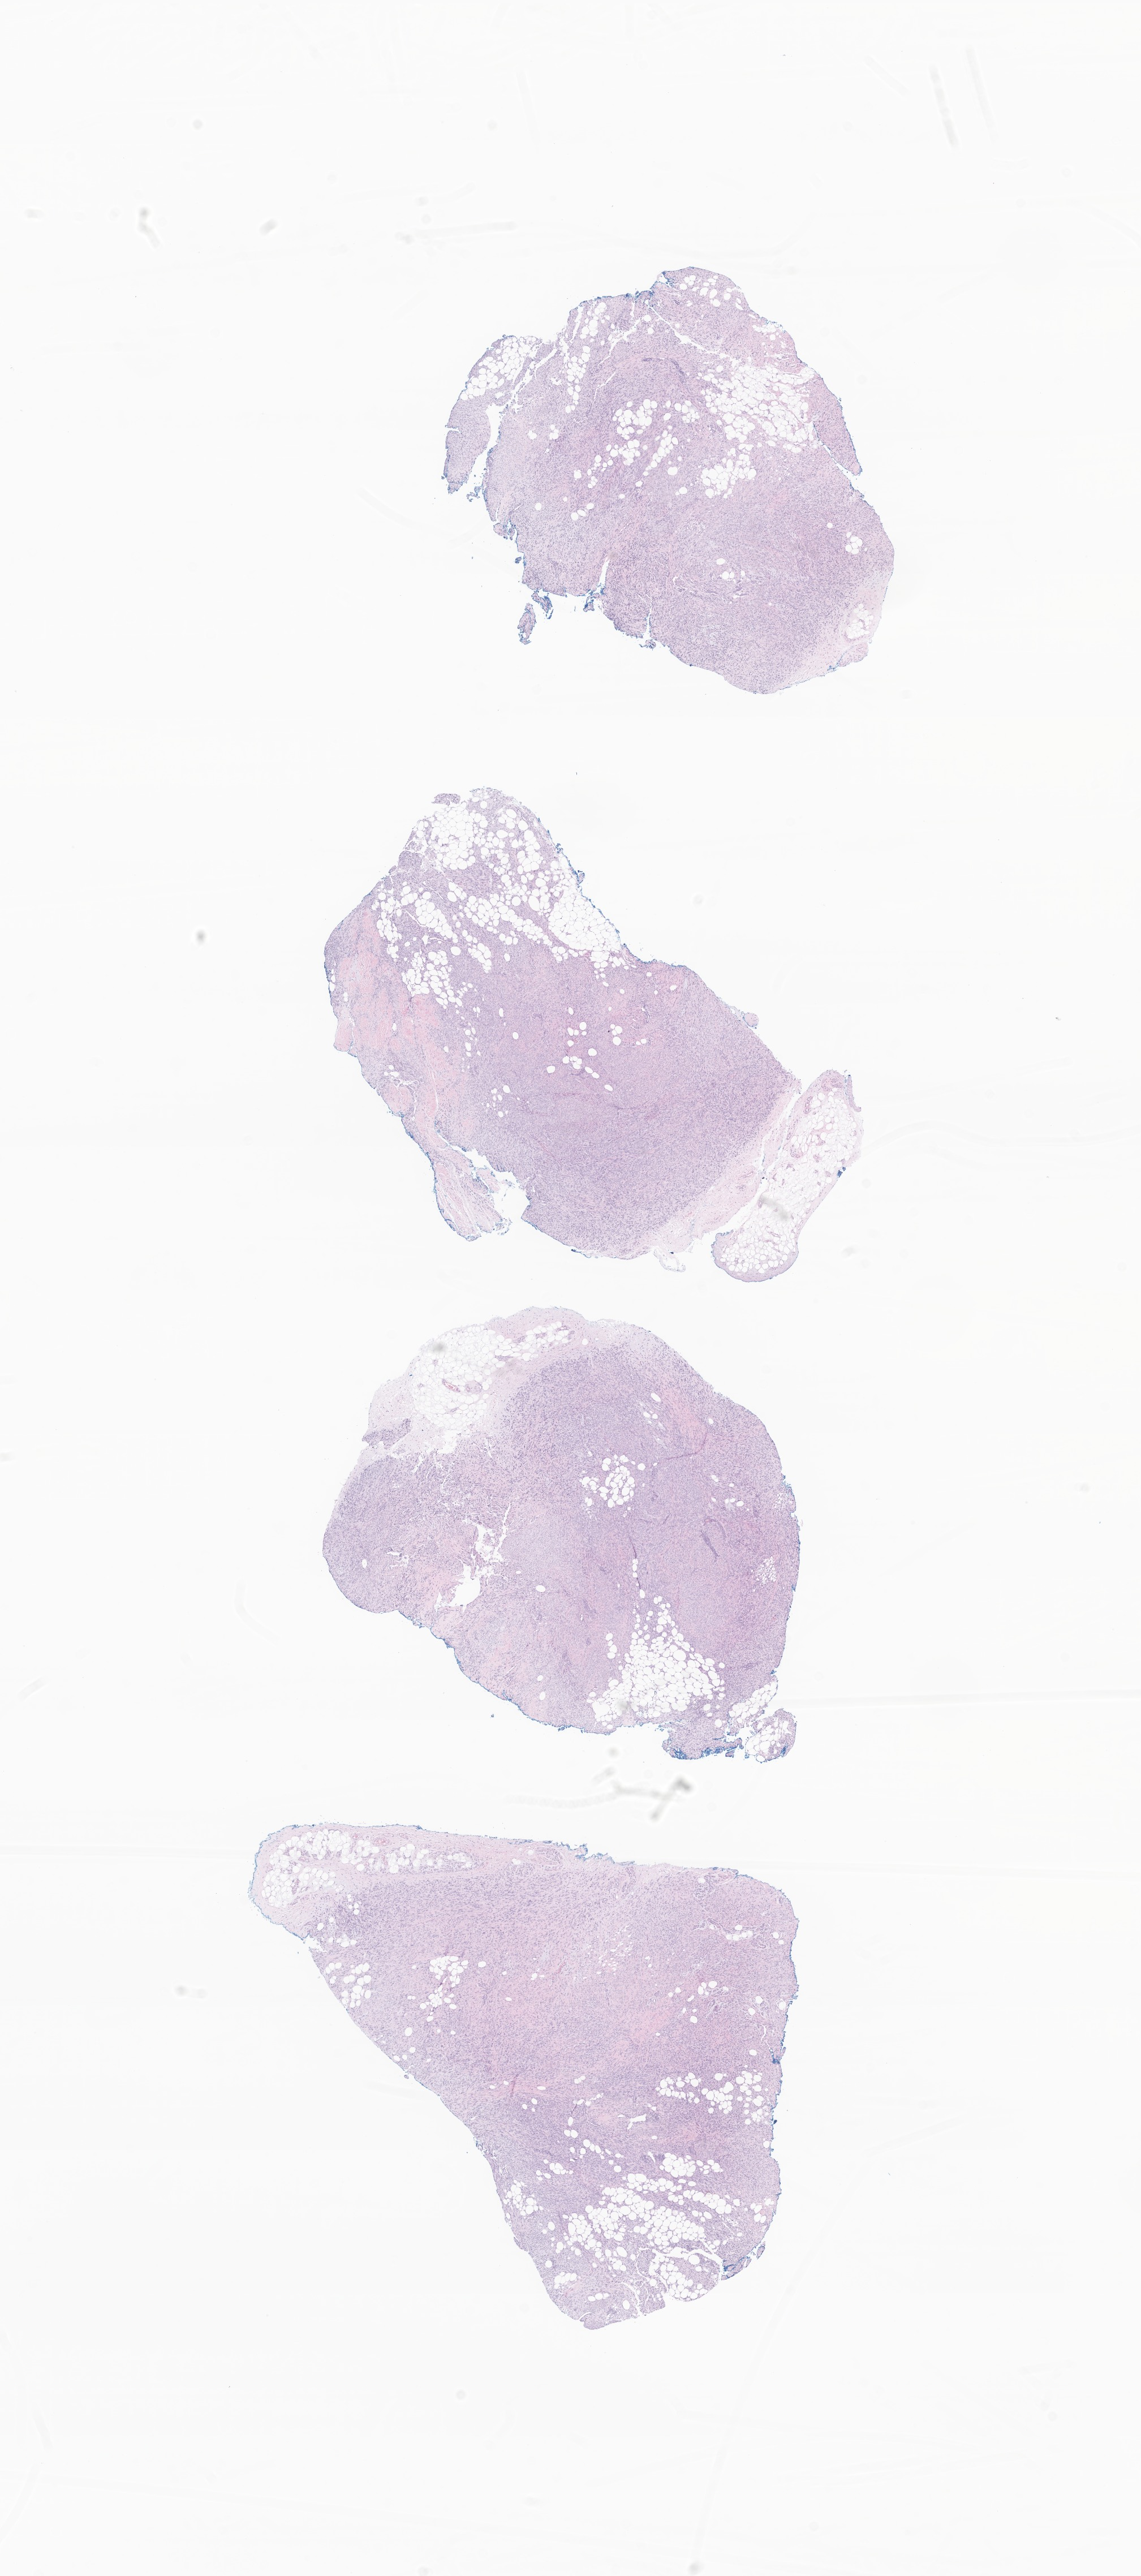
Digitized hematoxylin and eosin (H&E)-stained section of tumor tissue from the upper limb — shown as a low-resolution overview of the whole scanned area (about 8.5 x 19.2 mm). FFPE section. Patient: male, age 76 months.
Diagnosis: Malignant tumor, spindle cell type.